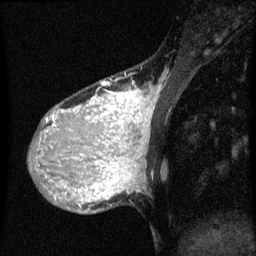
Breast MRI (dynamic contrast-enhanced), one sagittal slice. Position 14 of 60 along the scan axis. Dynamic contrast-enhanced series, image 2 of 3 at this slice position (ordered by acquisition). 1.5 T. TE 4.2 ms, TR 8 ms. 2 mm slice thickness. 256 × 256 image matrix, field of view 180 × 180 mm. Patient: female, 36 years.
Outlined on this slice (semi-automatically segmented with operator editing):
- analysis volume of interest (the breast-tissue region the enhancement analysis was run in; not a lesion): bounding box <32,78,157,161> (left, top, right, bottom; pixels)
- tumour enhancement mask (voxels above the 70 % enhancement threshold inside the analysis volume of interest): <40,82,155,161>